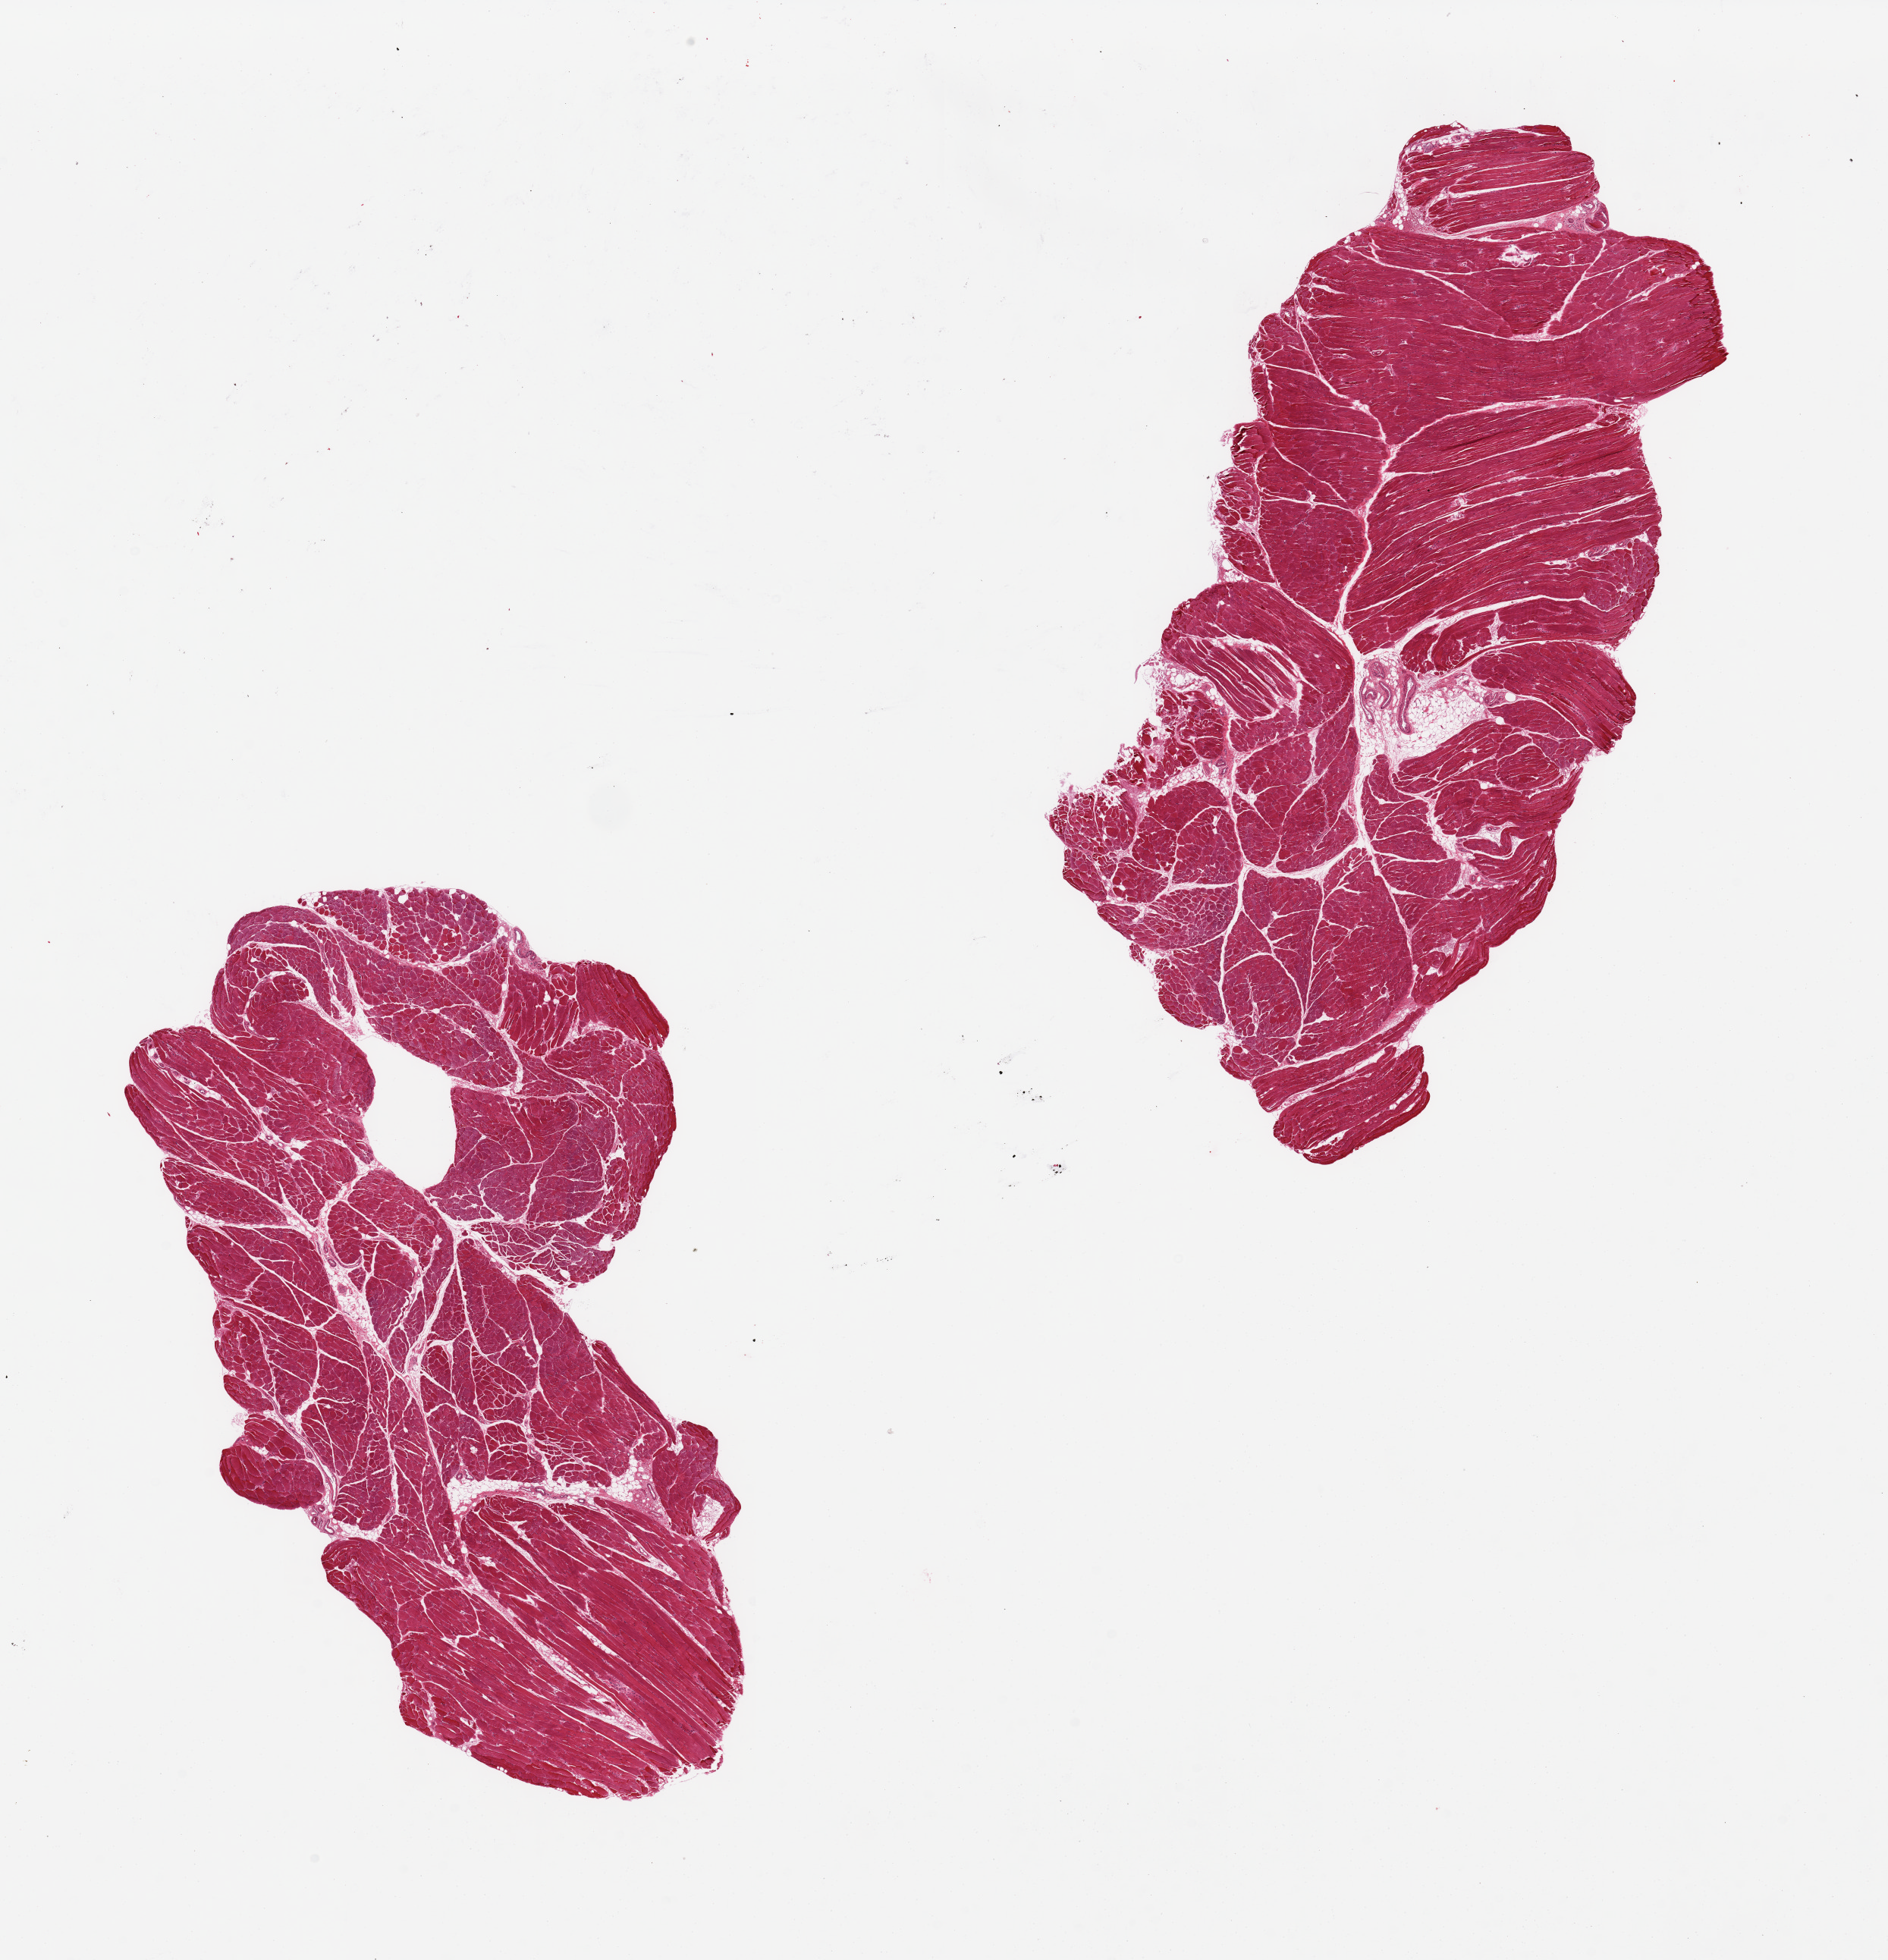
Haematoxylin and eosin whole-slide image — whole scanned area (about 19.7 x 20.4 mm, slide scanned at 20x) shown as a low-resolution overview, PAXgene-fixed, paraffin-embedded tissue, section of skeletal muscle (target tissue), tissue donor sample.
Pathologist's review note for this sample: 2 pieces.